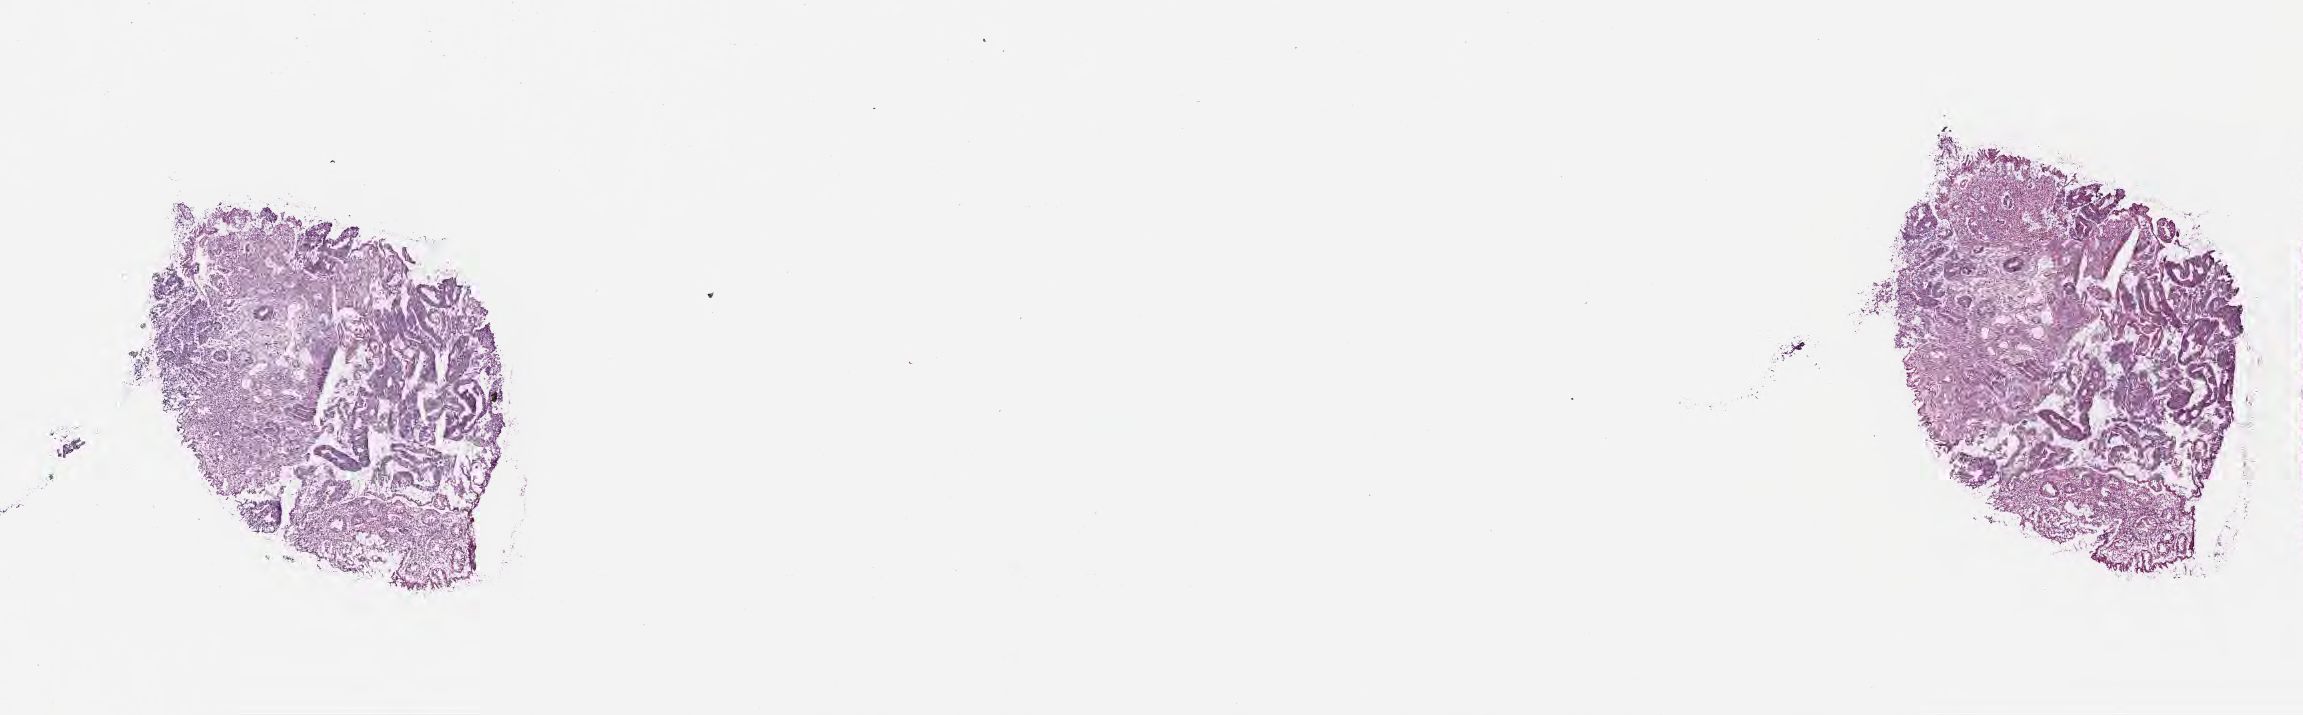
Haematoxylin and eosin whole-slide image, shown as a low-resolution overview of the whole scanned area (about 18.6 x 5.8 mm), cryosection, specimen: primary tumor, anatomic site: sigmoid colon. Patient: female, age at initial diagnosis 60 years. Tumor grade: G2 (moderately differentiated). Pathologist review of this section (percent, as recorded): tumor cells 75%, tumor nuclei 75%, stromal cells 25%, necrosis 0%, normal cells 0%. Inflammatory infiltration, as recorded: lymphocyte infiltration 7%, monocyte infiltration 2%, neutrophil infiltration 9%.
AJCC pathologic stage: Stage IIIB. Histologic diagnosis: Adenocarcinoma, NOS.